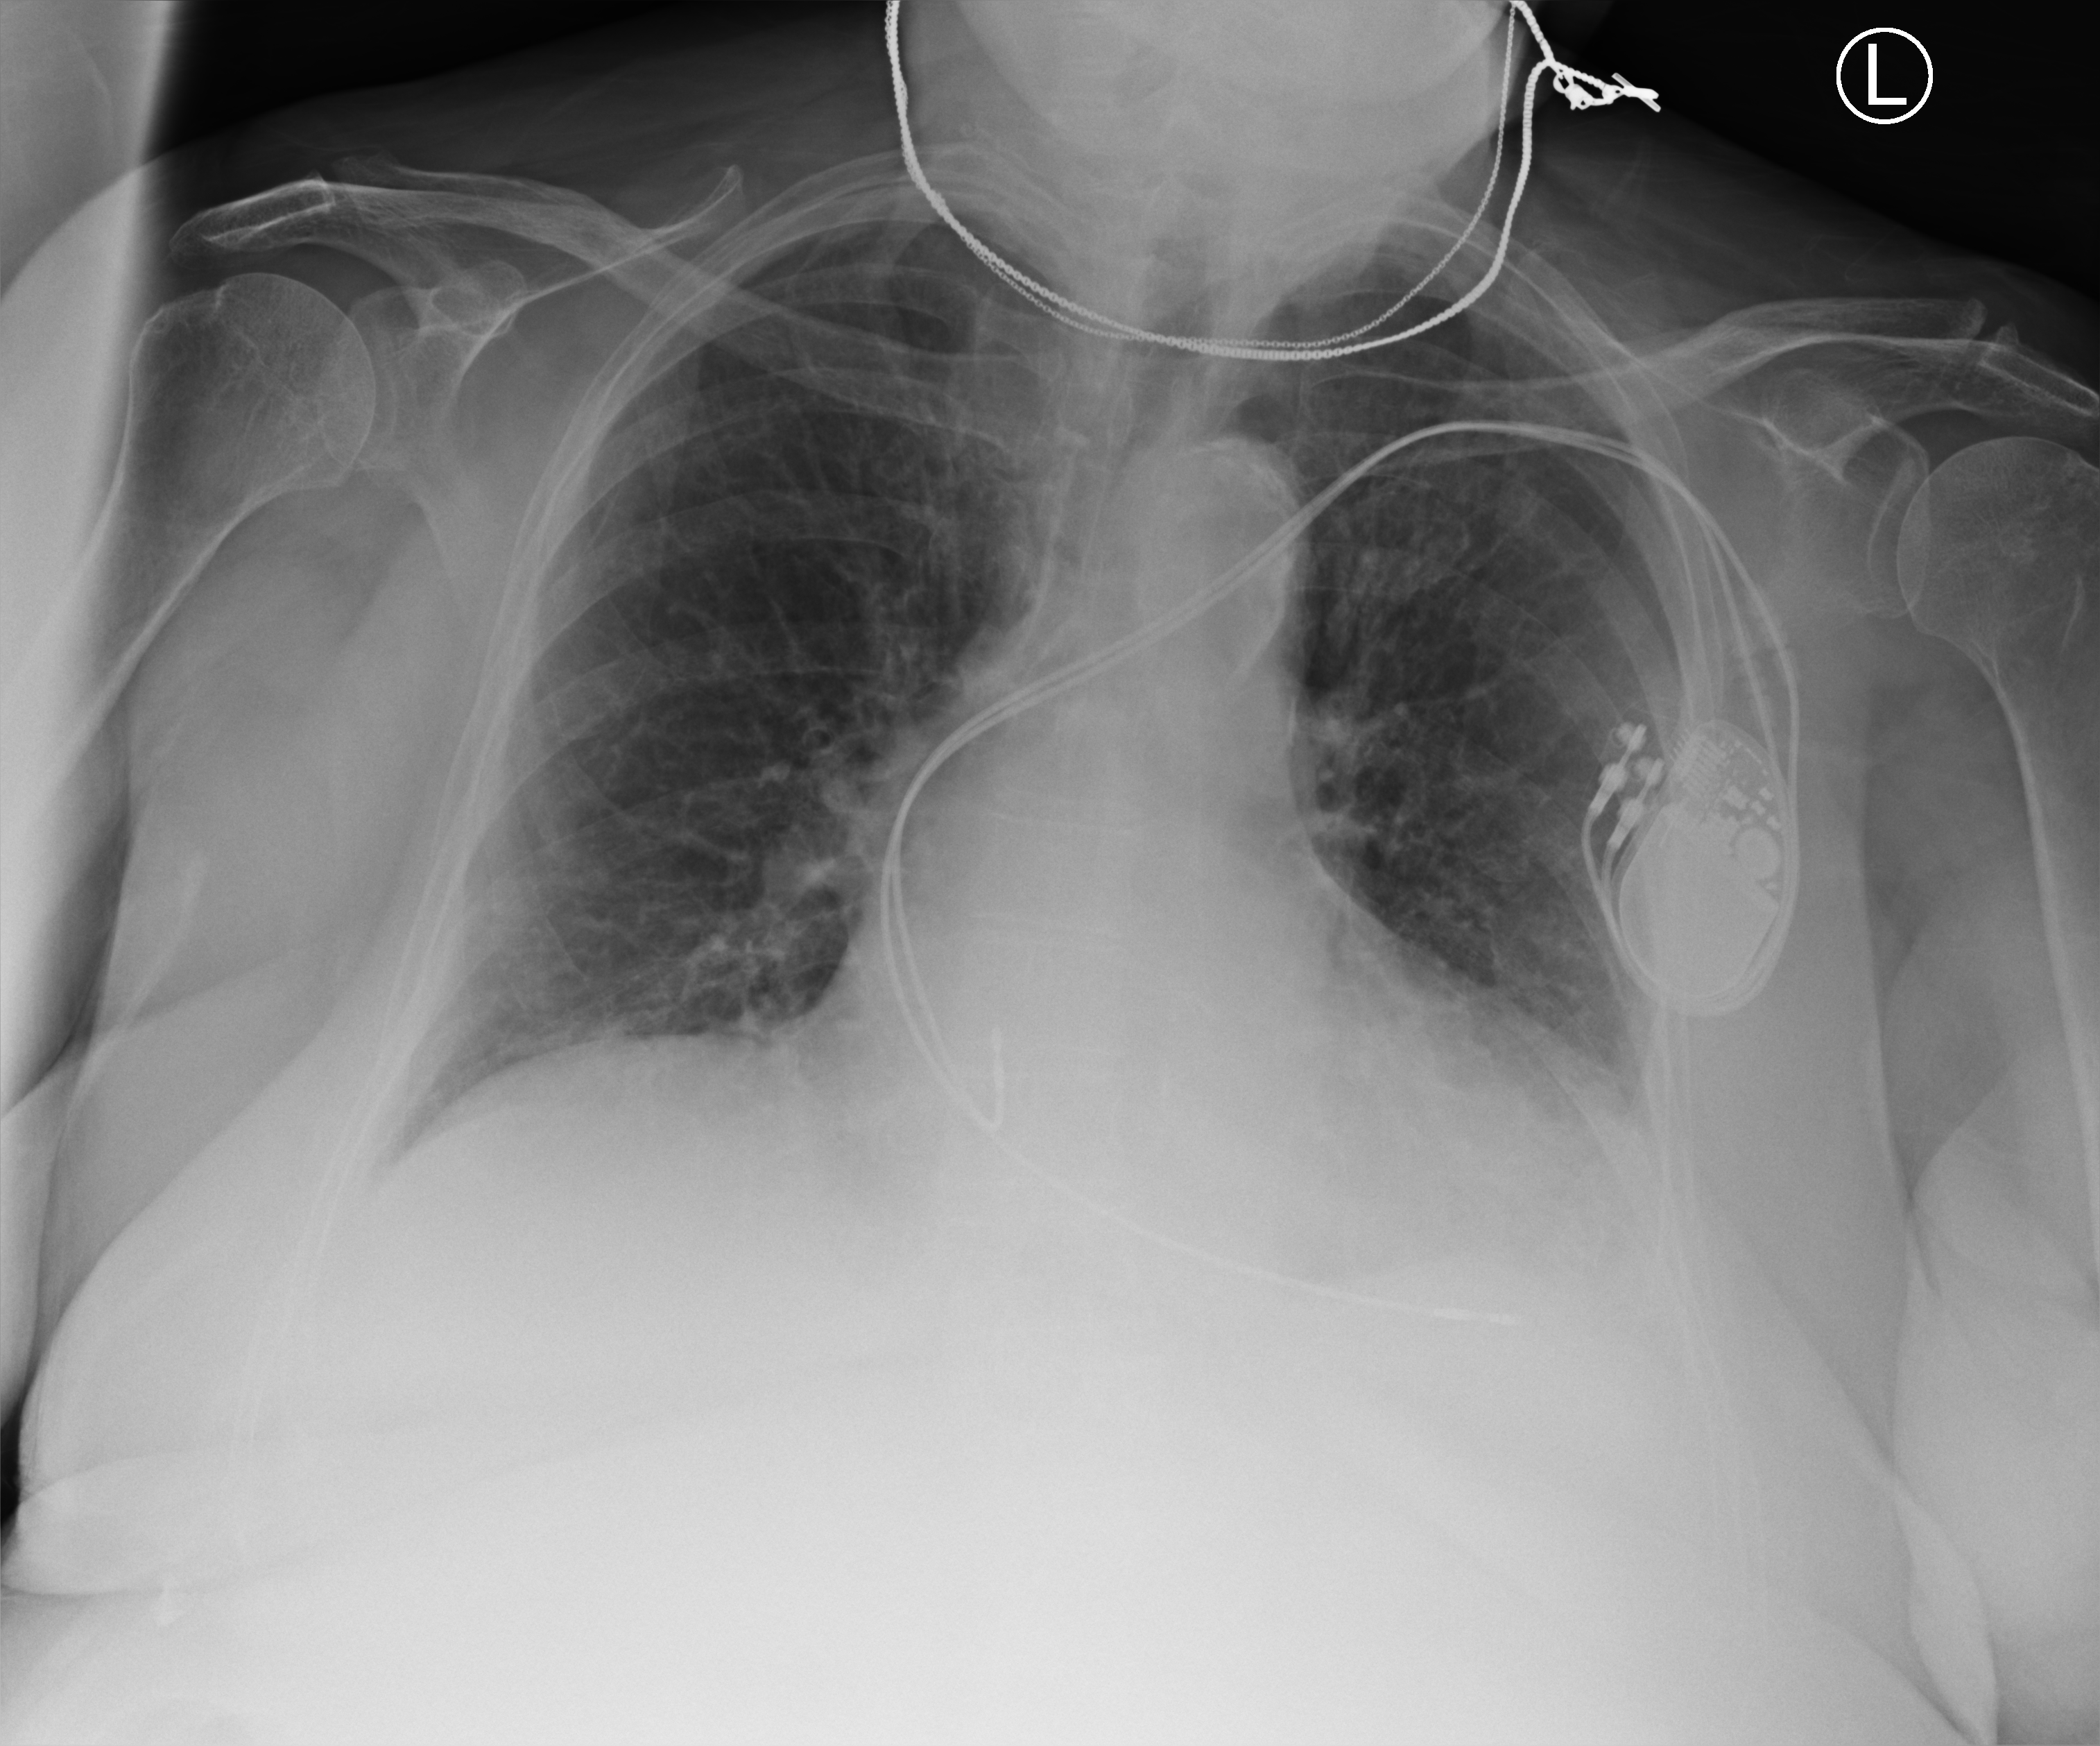
Portable chest radiograph. Patient hospitalised with COVID-19; female, aged 75–90 years.
Hospital-stay facts (about this admission, not read from this image; timing relative to this image not recorded): mechanically ventilated during this hospital stay: no.